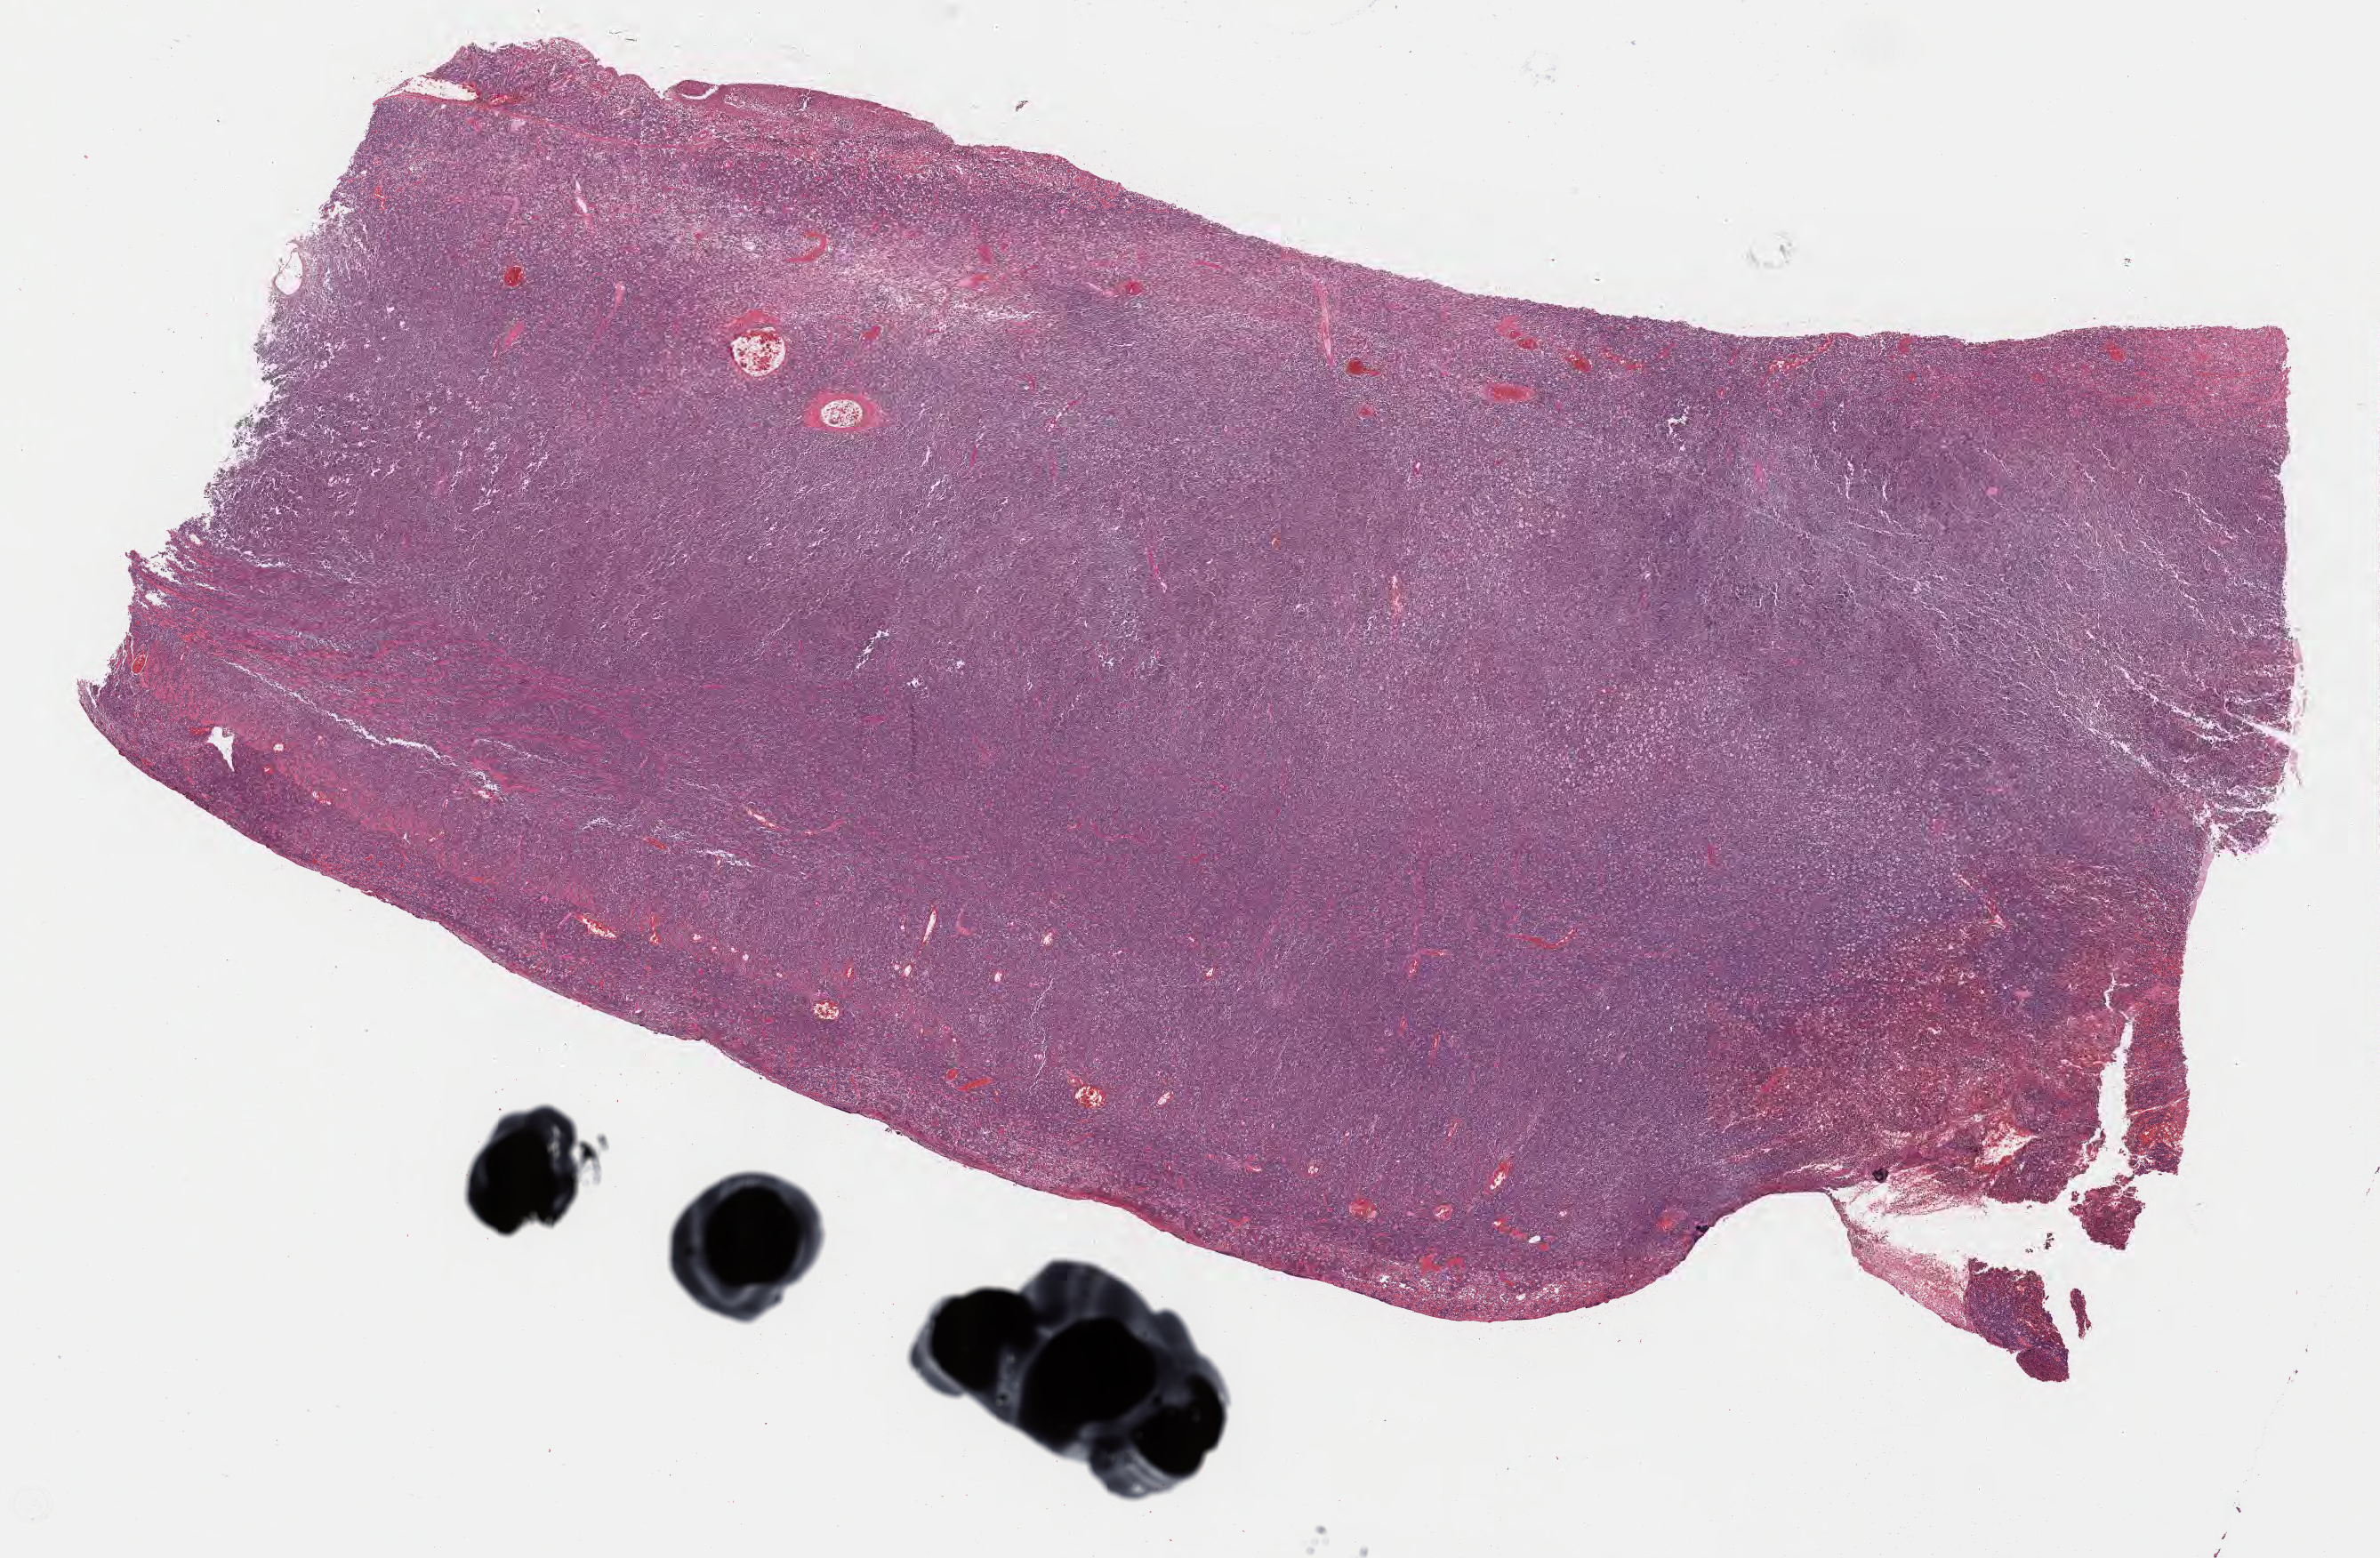
Digitized H&E-stained section, a low-resolution overview of the entire scanned area, about 21.6 x 14.2 mm; tumor tissue. Patient: female, age at initial diagnosis 6 years.
Diagnosis: Burkitt lymphoma, NOS.